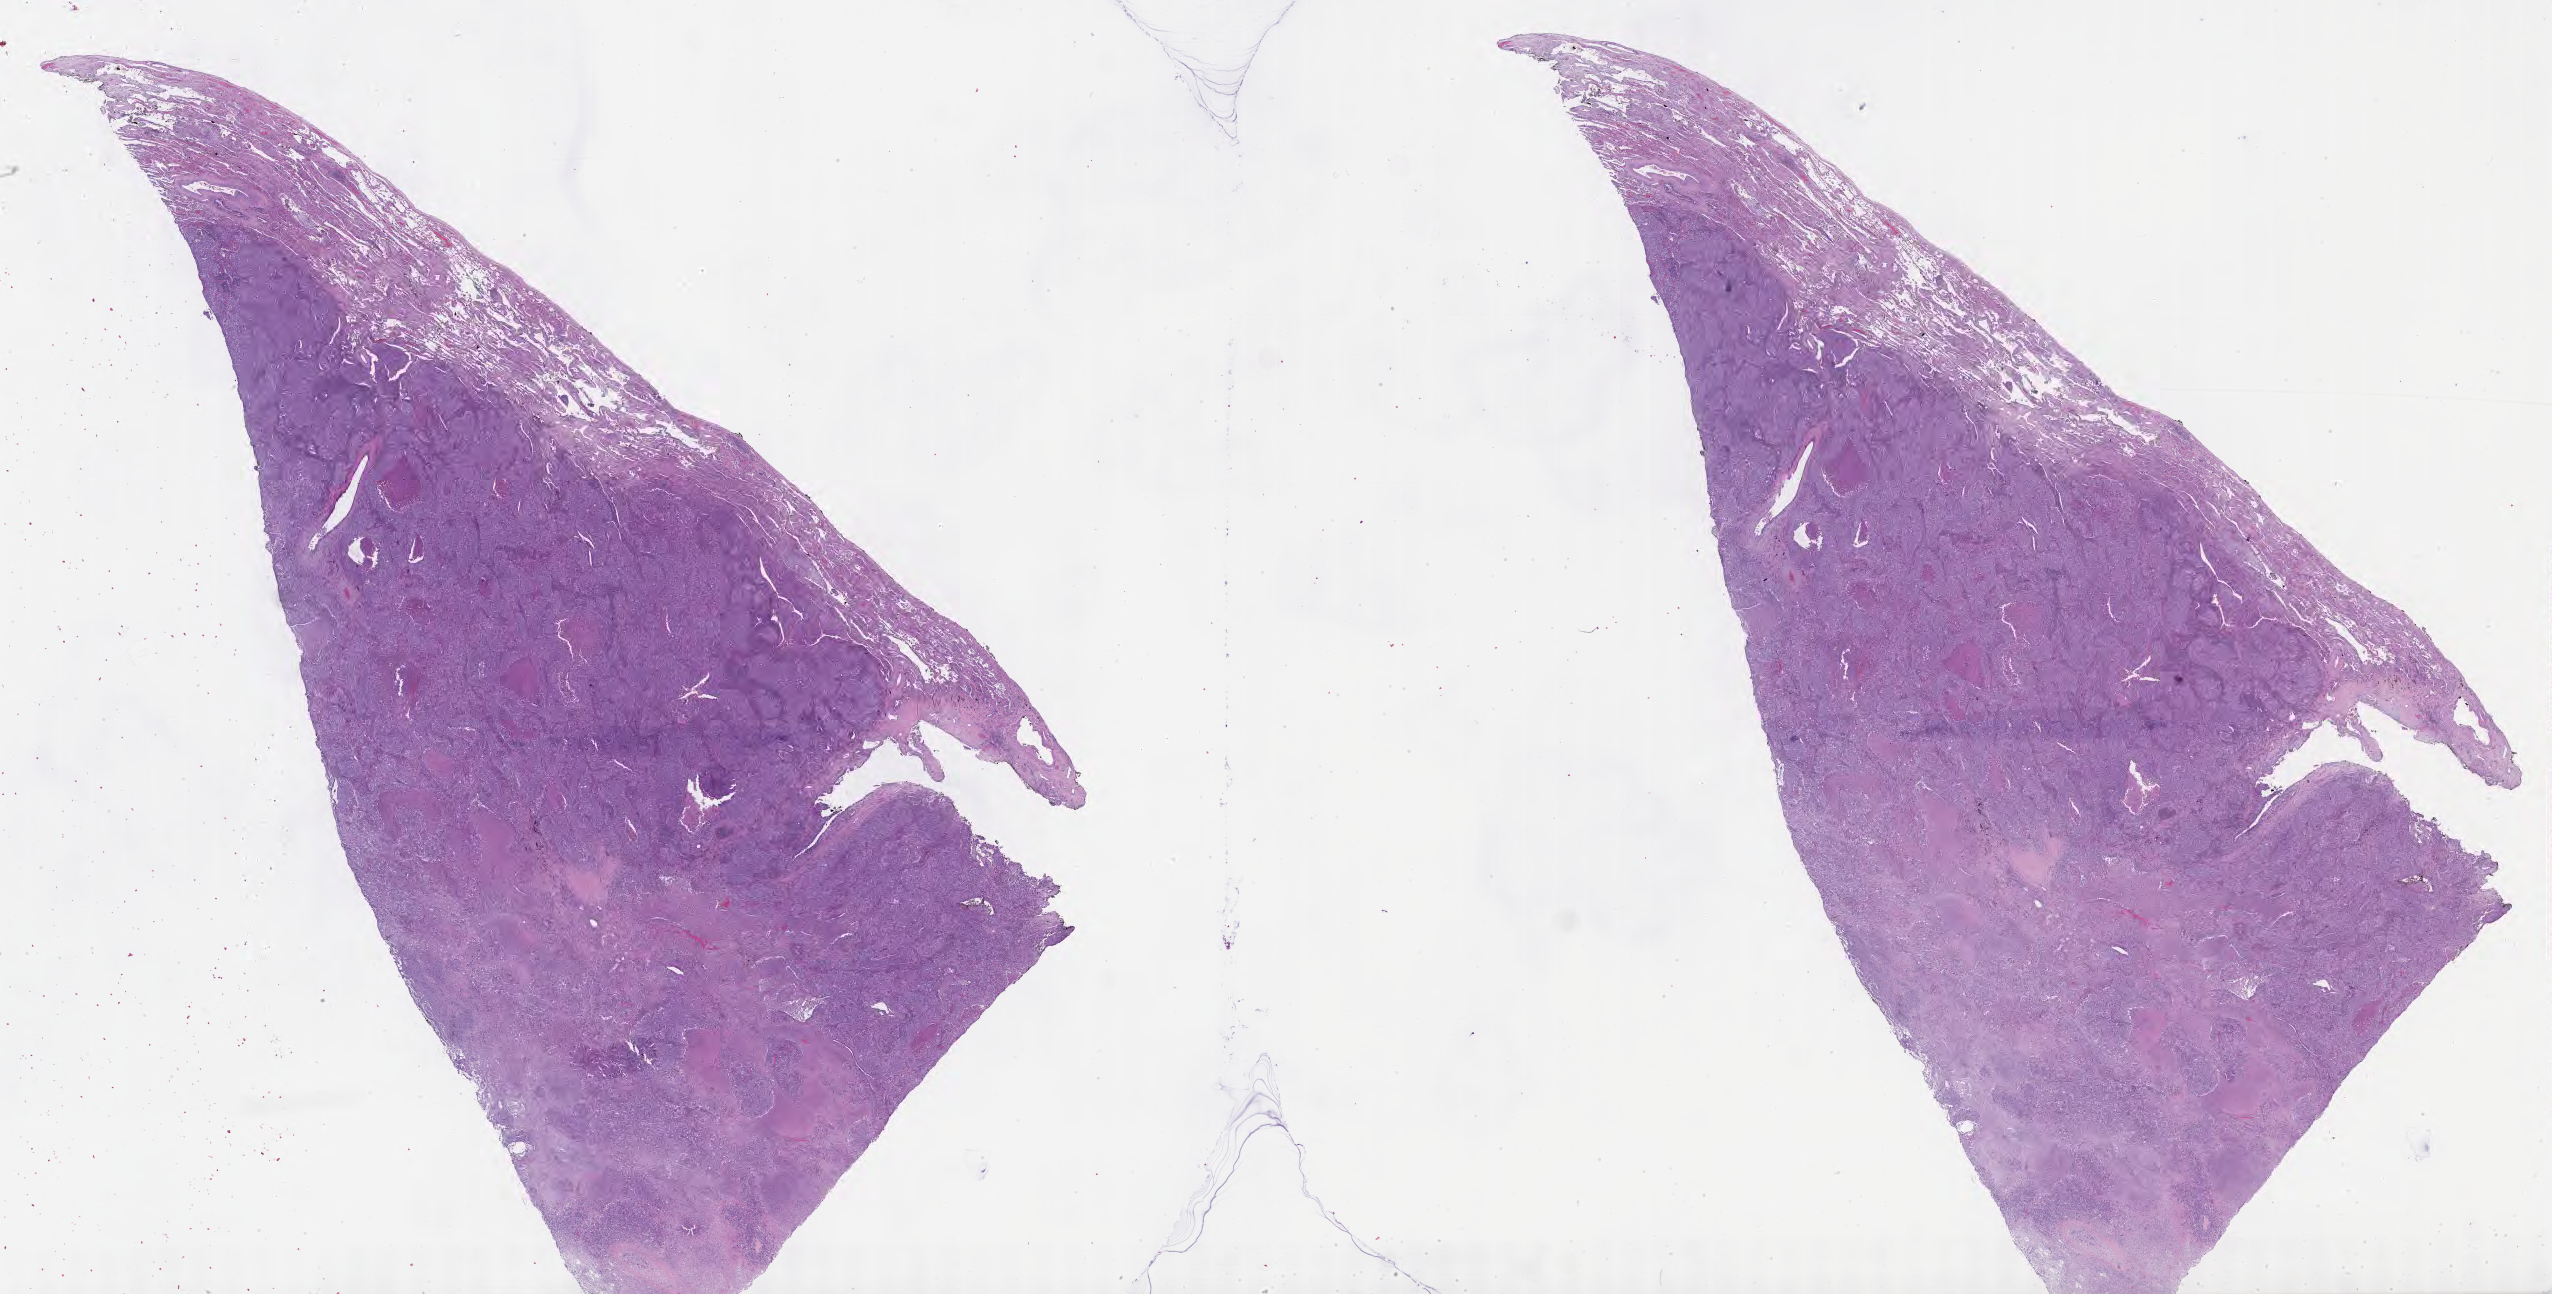
Haematoxylin and eosin whole-slide image — a low-resolution overview of the entire scanned area, about 41.3 x 20.9 mm, specimen: tumor tissue, site: lung (left). Patient: female, aged 69.
Histologic diagnosis: Squamous cell carcinoma, NOS.